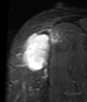
MRI of an extremity soft-tissue mass, one axial slice; slice 32 of 48 in the series (ordered by position); STIR; MR volume resampled by the dataset authors to the PET/CT grid (not the native acquisition matrix); 3.27 mm slice thickness; 87 × 102 image matrix, field of view 85 × 100 mm. Female patient. From the clinical record (not read from this slice): histological type: synovial sarcoma; grade: intermediate; site of the primary tumour: right thigh.
Annotated regions visible in this slice (expert contour drawn on MRI and transferred to this co-registered scan by the dataset authors):
- gross tumour volume including surrounding oedema: bounding box <24,31,55,71> (left, top, right, bottom; pixels)
- gross tumour volume (mass): <24,34,50,71>